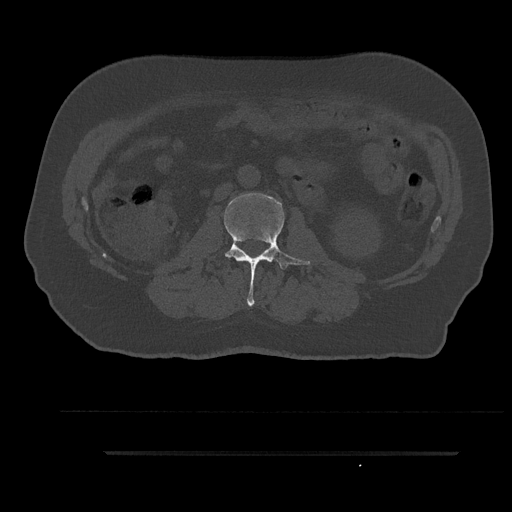
CT including the spine, one axial slice; position 104 of 797 along the scan axis; reconstruction kernel Br40s/3; bone window (W 1800 / L 400 HU); 512 × 512 image matrix. Patient: male, 63 years. Case-level facts recorded for this patient, not image findings: primary cancer: renal; vertebrae with lytic lesions (as recorded): T8.
Outlined on this slice (semi-automatic segmentation, software-assisted and operator-edited):
- L2 vertebra: box from (x=224, y=193) to (x=310, y=306) px